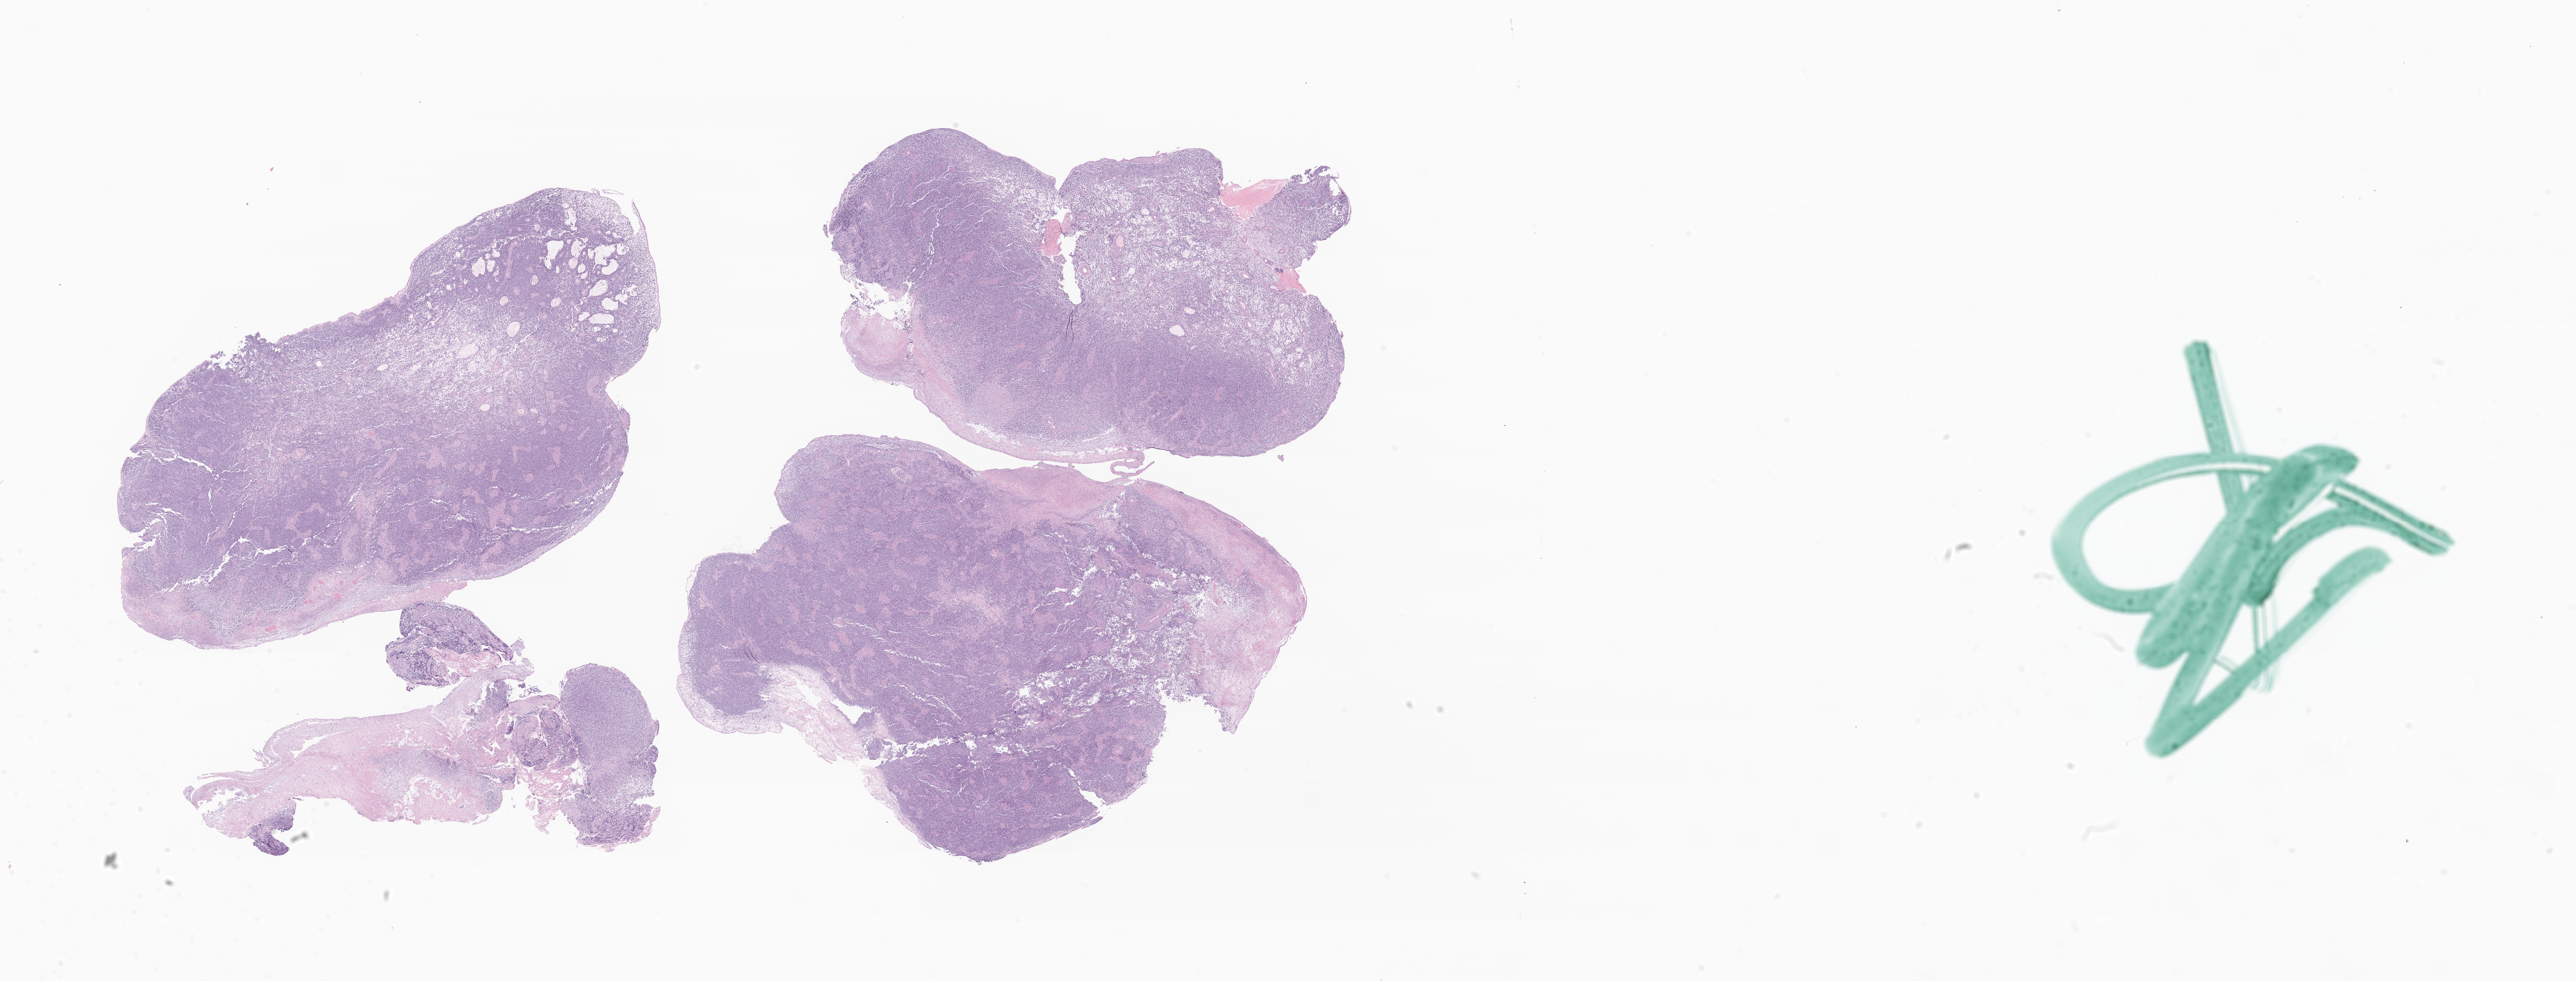
Whole-slide image, hematoxylin and eosin (H&E) stain of tumor tissue from the soft tissues of head and neck, low-resolution overview of the scanned area, about 41.7 x 15.9 mm; FFPE section. Male patient, age 48 months.
Diagnosis: Embryonal rhabdomyosarcoma, NOS.